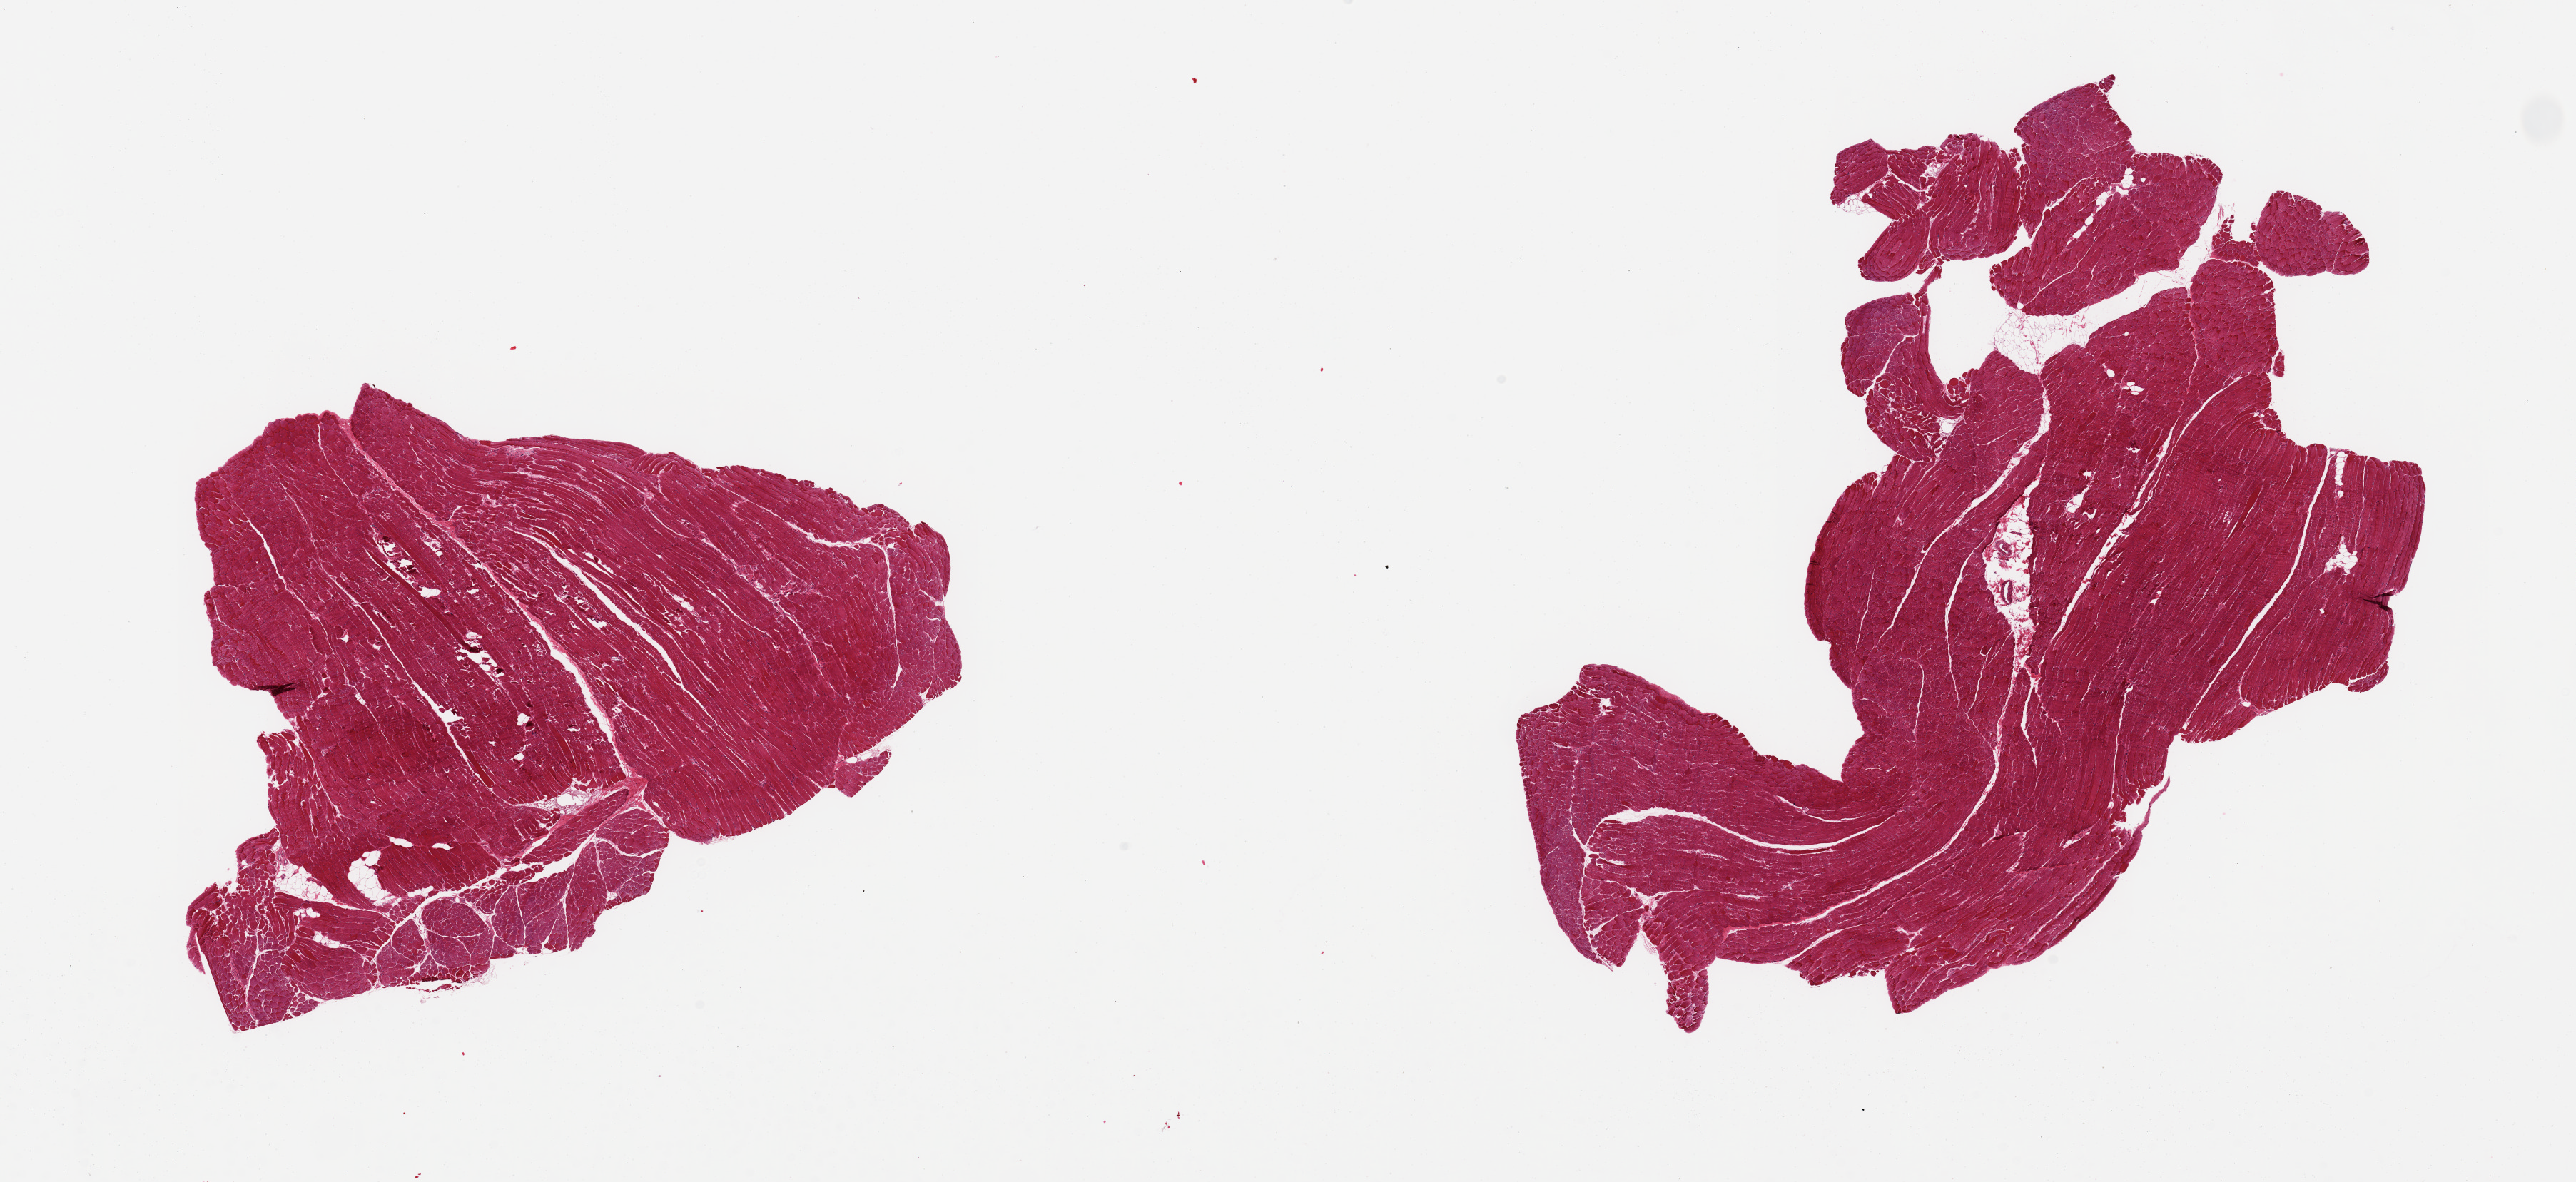
H&E whole-slide image, whole scanned area (about 28.5 x 13.1 mm, acquisition: 20x scan) shown as a low-resolution overview. PAXgene-fixed, paraffin-embedded tissue. Section of skeletal muscle (target tissue). Tissue donor sample. Donor: female.
Review note (as recorded): 2 pieces, minimal internal fat.